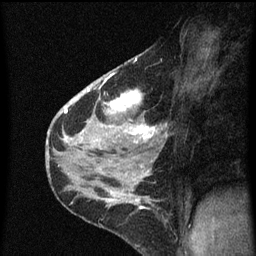
Breast MRI (dynamic contrast-enhanced), one sagittal slice. Position 40 of 60 along the scan axis. Dynamic contrast-enhanced series, image 2 of 3 at this slice position (ordered by acquisition). 1.5 T. TE 4.2 ms, TR 8 ms. 2 mm slice thickness. 256 × 256 image matrix, field of view 180 × 180 mm. Patient: female, 38 years.
Structures marked on this image (semi-automatic segmentation, software-assisted and operator-edited):
- analysis volume of interest (the breast-tissue region the enhancement analysis was run in; not a lesion): bounding box <80,56,169,151> (left, top, right, bottom; pixels)
- tumour enhancement mask (voxels above the 70 % enhancement threshold inside the analysis volume of interest): <82,58,159,143>